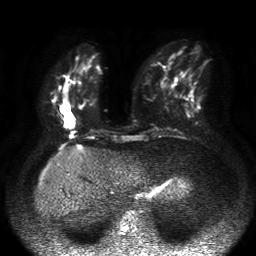
Breast MRI, one axial slice. Diffusion-weighted series; image 2 of 4 stored at this slice position (different b-values; order by instance number). 1.5 T. 4 mm slice thickness. 256 × 256 image matrix, field of view 360 × 360 mm. Female patient.
Outlined on this slice (manually delineated by an expert):
- tumour on diffusion-weighted imaging: bounding box (x1, y1, x2, y2) in pixels: (63, 114, 76, 128)